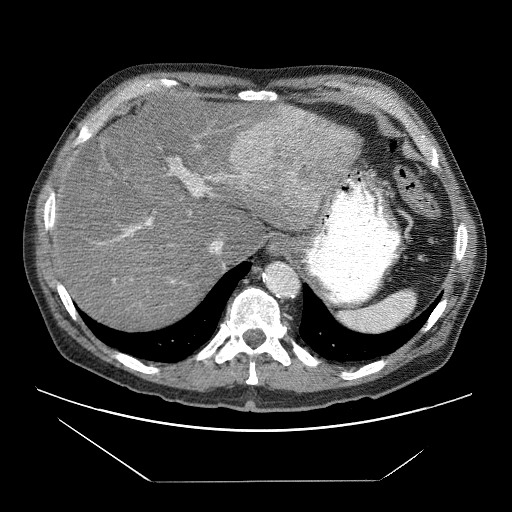
Contrast-enhanced abdominal CT (liver protocol), one axial slice. Slice 54 of 83 in the series (ordered by position). Reconstruction kernel STANDARD. Soft-tissue window (W 400 / L 40 HU). 2.5 mm slice thickness. 512 × 512 image matrix, field of view 420 × 420 mm. Case-level facts recorded for this patient, not image findings: diagnosis: hepatocellular carcinoma (patient treated with transarterial chemoembolisation; whether this scan precedes or follows treatment is not stated here); TNM stage (as recorded): Stage-IVB; Child-Pugh class: B; tumour differentiation: poorly differentiated.
Annotated regions visible in this slice (semi-automatic segmentation, software-assisted and operator-edited):
- liver parenchyma outside the tumour (the mass and vessels are separate outlines, so this box may not span the whole liver): bounding box [x1, y1, x2, y2] px = [52, 93, 360, 326]
- mass: [232, 102, 359, 227]
- liver vessels: [54, 145, 243, 283]